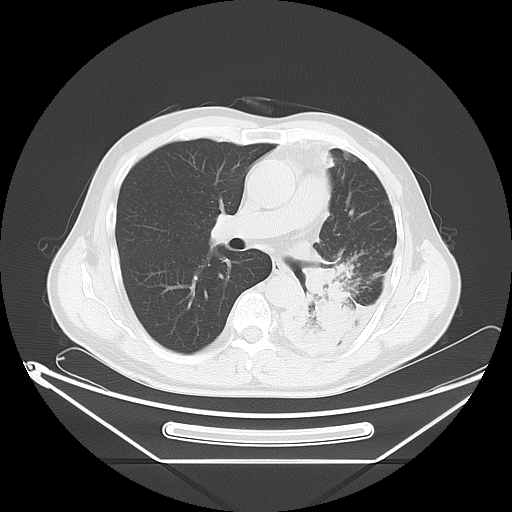
Chest CT, one axial slice. Slice 36 of 63 in the series (ordered by position). 120 kVp. Lung window (W 1500 / L -600 HU). 5 mm slice thickness. 512 × 512 image matrix, field of view 442 × 442 mm. Patient: male, 60 years. Case-level facts recorded for this patient, not image findings: clinical TNM (as recorded): T4 N1 M1.
Annotated regions visible in this slice (bounding box drawn by a radiologist):
- lung tumour (recorded histology: adenocarcinoma): bounding box <292,256,348,345> (left, top, right, bottom; pixels)